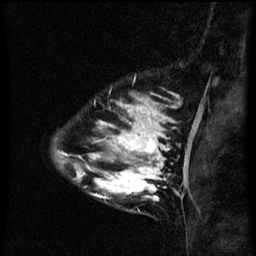
Breast MRI (dynamic contrast-enhanced), one sagittal slice; position 15 of 60 along the scan axis; dynamic contrast-enhanced series, image 2 of 3 at this slice position (ordered by acquisition); 1.5 T; TE 4.2 ms, TR 8 ms; 2.3 mm slice thickness; 256 × 256 image matrix, field of view 180 × 180 mm. Female patient, age 33 years.
Annotated regions visible in this slice (semi-automatically segmented with operator editing):
- analysis volume of interest (the breast-tissue region the enhancement analysis was run in; not a lesion): bounding box <71,118,171,201> (left, top, right, bottom; pixels)
- tumour enhancement mask (voxels above the 70 % enhancement threshold inside the analysis volume of interest): <76,118,171,201>